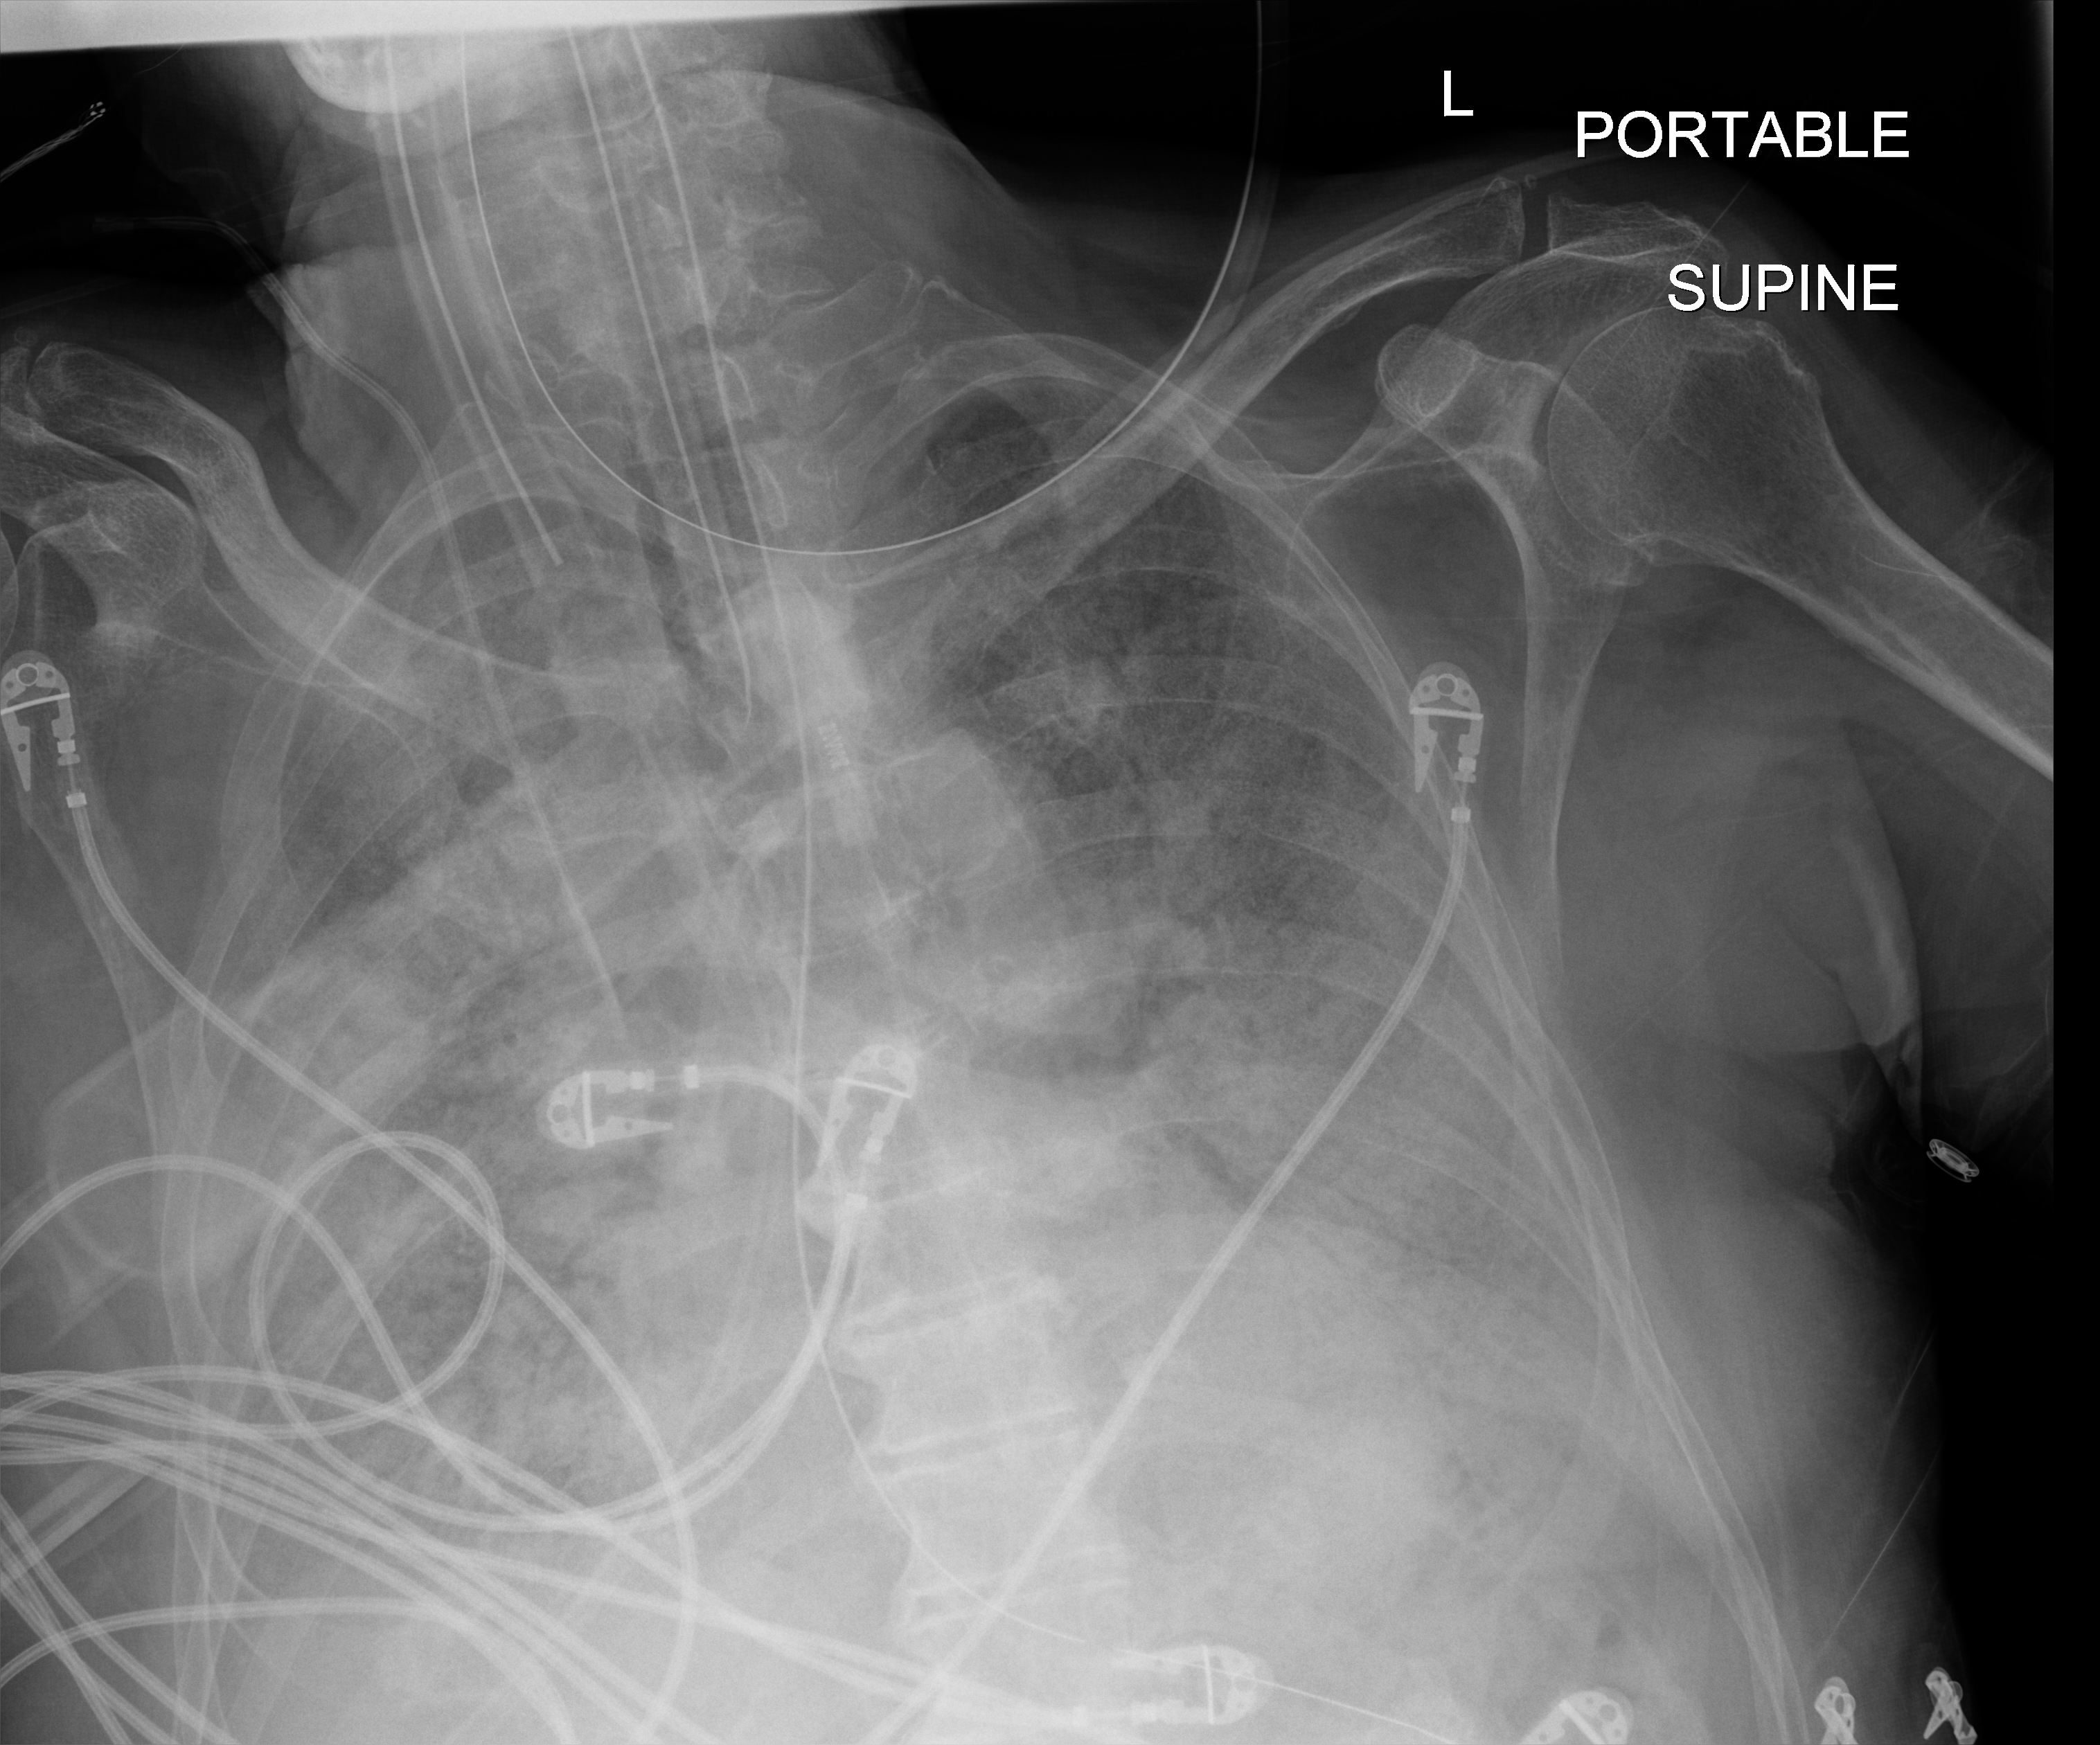
Portable chest radiograph; anteroposterior (AP) projection. Male patient hospitalised with COVID-19, age 75–90 years.
From the hospital-stay record, not from the radiograph (when in the stay this image was taken is not recorded):
- hypertension (admission record): no
- diabetes (admission record): no
- admitted to intensive care during this hospital stay: yes